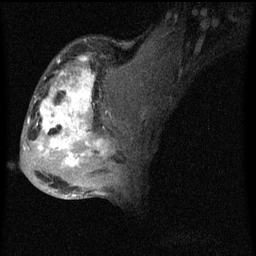
Breast MRI (dynamic contrast-enhanced), one sagittal slice. Position 31 of 60 along the scan axis. Dynamic contrast-enhanced series, image 2 of 4 at this slice position (ordered by acquisition). 1.5 T. TE 4.2 ms, TR 8 ms. 2 mm slice thickness. 256 × 256 image matrix, field of view 180 × 180 mm. Female patient, age 50 years.
Structures marked on this image (semi-automatically segmented with operator editing):
- analysis volume of interest (the breast-tissue region the enhancement analysis was run in; not a lesion): box from (x=26, y=44) to (x=124, y=177) px
- tumour enhancement mask (voxels above the 70 % enhancement threshold inside the analysis volume of interest): (x=28, y=56)–(x=114, y=167)